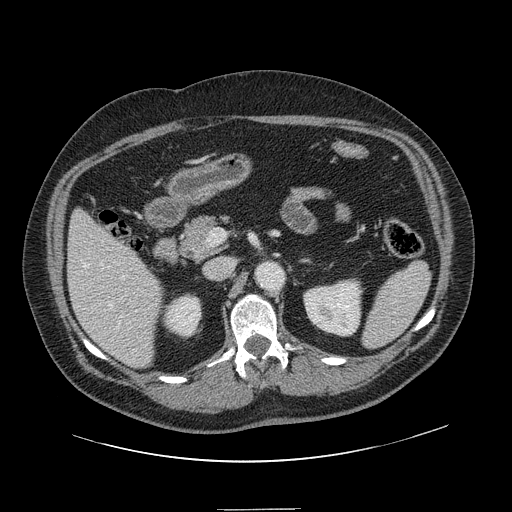
Contrast-enhanced abdominal CT, one axial slice. Position 67 of 154 along the scan axis. Soft-tissue window (W 400 / L 40 HU). 2.5 mm slice thickness. 512 × 512 image matrix, field of view 451 × 451 mm. Male patient, age 61 years. Case-level facts recorded for this patient, not image findings: diagnosis: colorectal cancer liver metastases, imaged before liver resection; multiple liver metastases: yes; largest metastasis: 2.6 cm; disease in both lobes: yes.
Structures marked on this image (outlined manually by an expert reader):
- hepatic veins: bounding box [x1, y1, x2, y2] px = [83, 260, 122, 329]
- liver: [69, 211, 163, 368]
- planned liver remnant (the part of the liver to remain after resection): [69, 211, 163, 365]